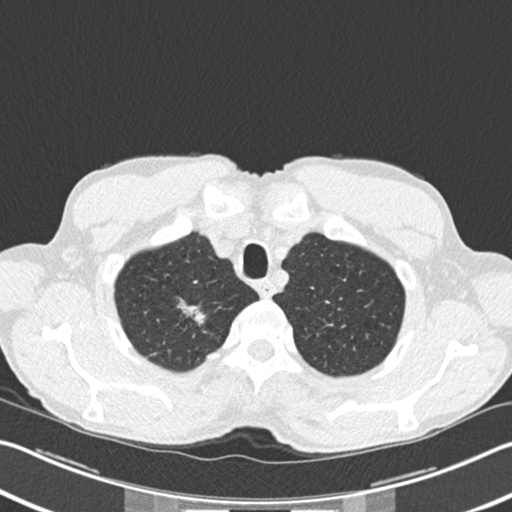
Chest CT (low-dose screening protocol), one axial image; second annual screen; lung window (W 1500 / L -600 HU); standard (soft-tissue) reconstruction kernel (B30f); slice 28 of 220 in the series. Male participant, aged 62 years at enrolment.
- Lesion marked by an expert reader, box from (x=169, y=294) to (x=211, y=340) px.
- The screening reader recorded 2 non-calcified nodules or masses ≥4 mm on this exam (right upper lobe, right upper lobe); which of them this box marks is not recorded.
- Lung cancer was diagnosed 5 days after this screen: bronchiolo-alveolar adenocarcinoma, NOS, right upper lobe, well differentiated (G1), stage IA (AJCC 6th edition), 15 mm at pathology.